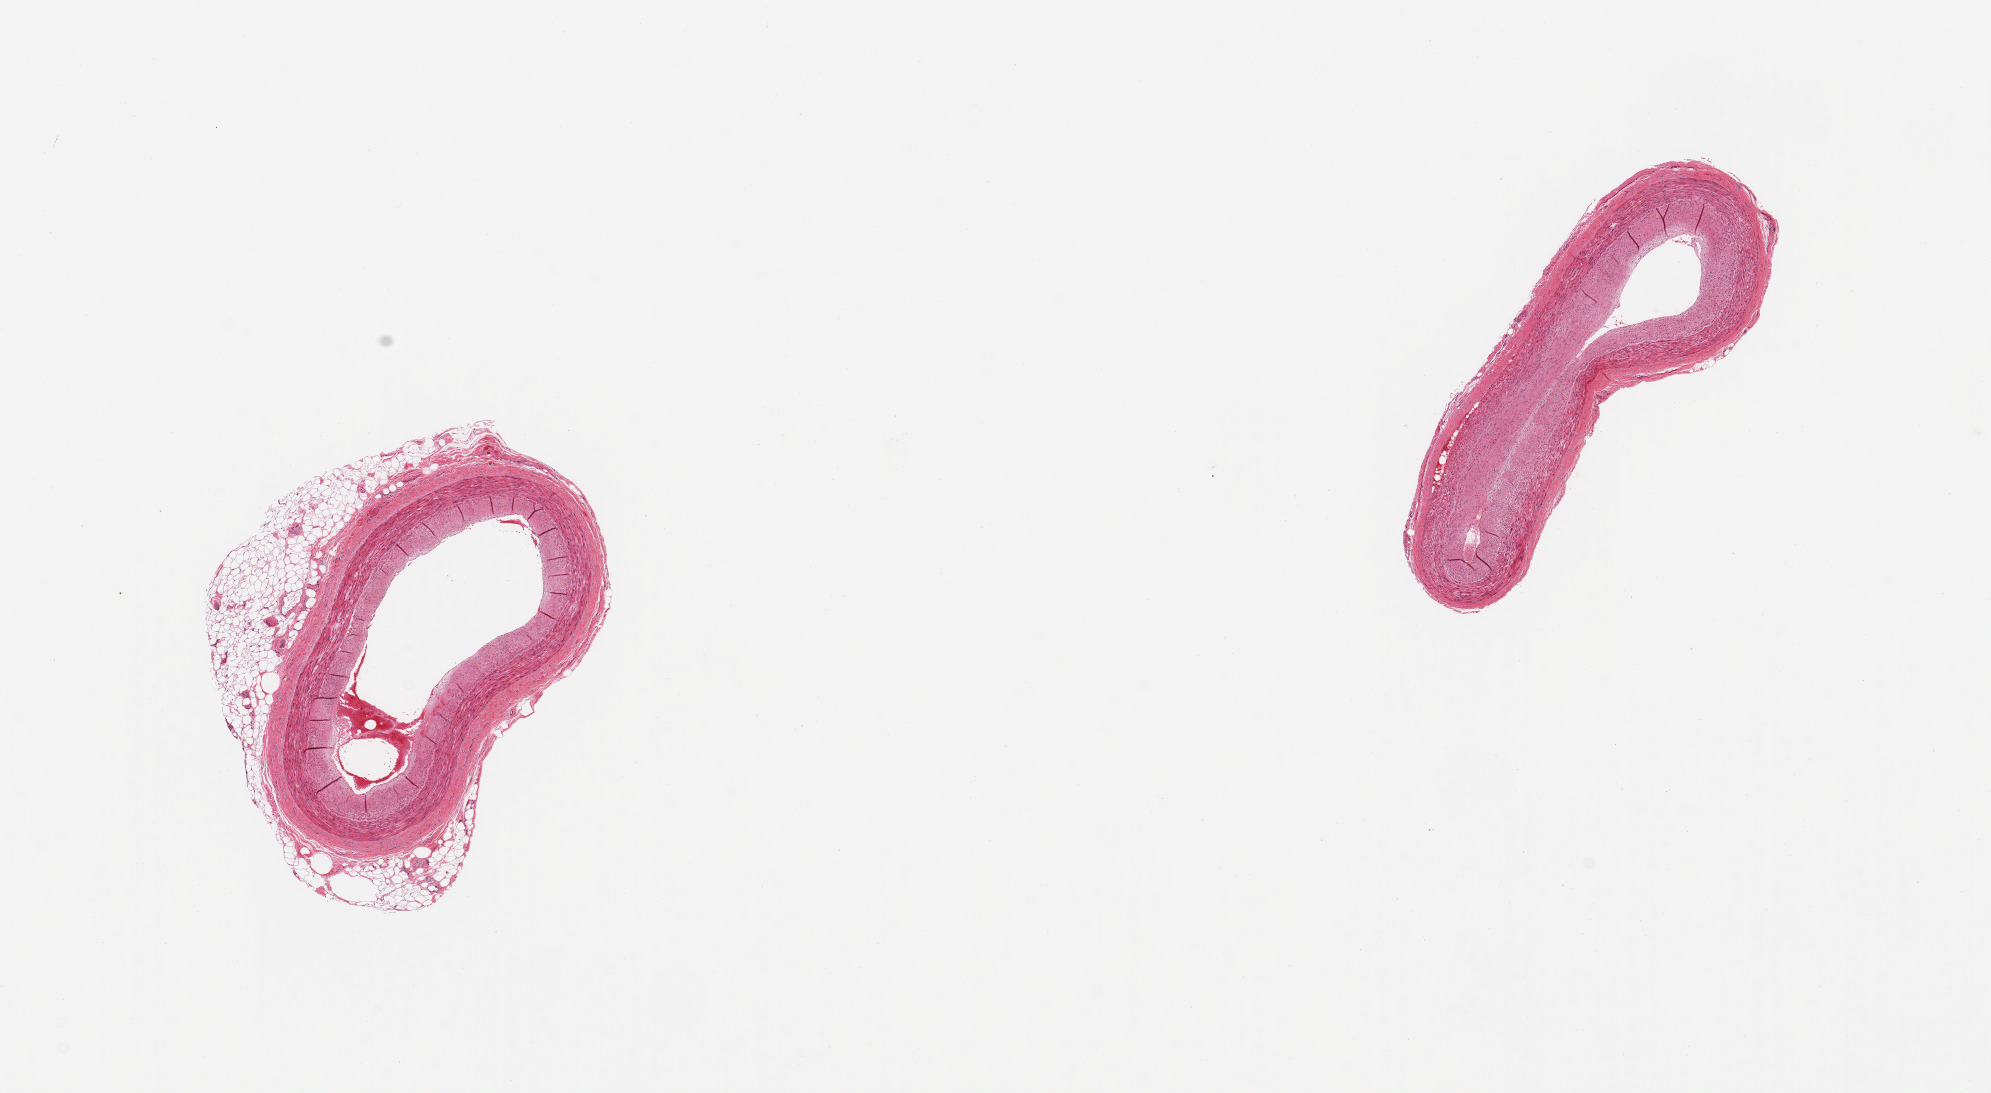
H&E whole-slide image, brightfield, shown as a low-resolution overview of the whole scanned area (about 15.8 x 8.6 mm). PAXgene-fixed, paraffin-embedded tissue. Target tissue: coronary artery. Donor tissue sample. Donor: female.
Reviewer comment on this tissue sample: 2 pieces, partial rim of adherent fat up to ~0.7mm.